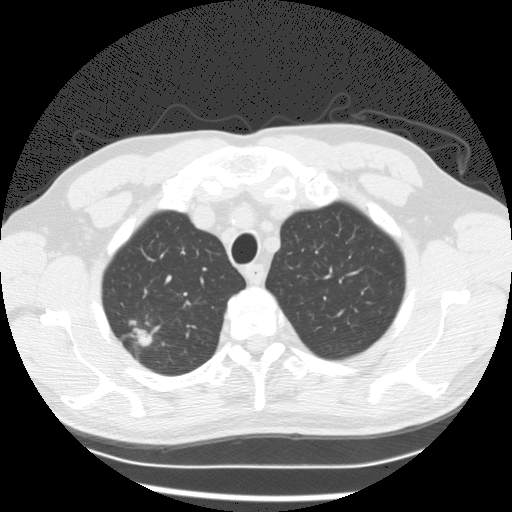
Low-dose screening chest CT, one axial slice. 120 kVp. Lung window (W 1500 / L -600 HU). 2.5 mm slice thickness. 512 × 512 image matrix, field of view 351 × 351 mm.
Outlined on this slice (manually delineated by an expert):
- lesion 1 (tumor, upper lobe of right lung): bounding box [x1, y1, x2, y2] px = [136, 330, 152, 346]